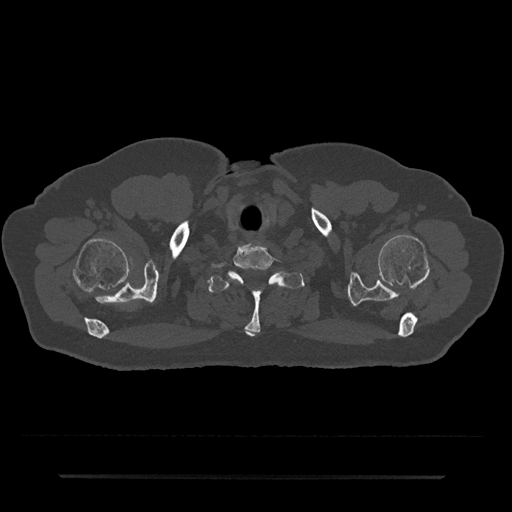
CT including the spine, one axial slice; reconstruction kernel Br40s/3; bone window (W 1800 / L 400 HU); 512 × 512 image matrix, field of view 437 × 437 mm. Patient: male, 69 years. Case-level facts recorded for this patient, not image findings: primary cancer: prostate.
Structures marked on this image (semi-automatically segmented with operator editing):
- T1 vertebra: box from (x=208, y=272) to (x=304, y=337) px